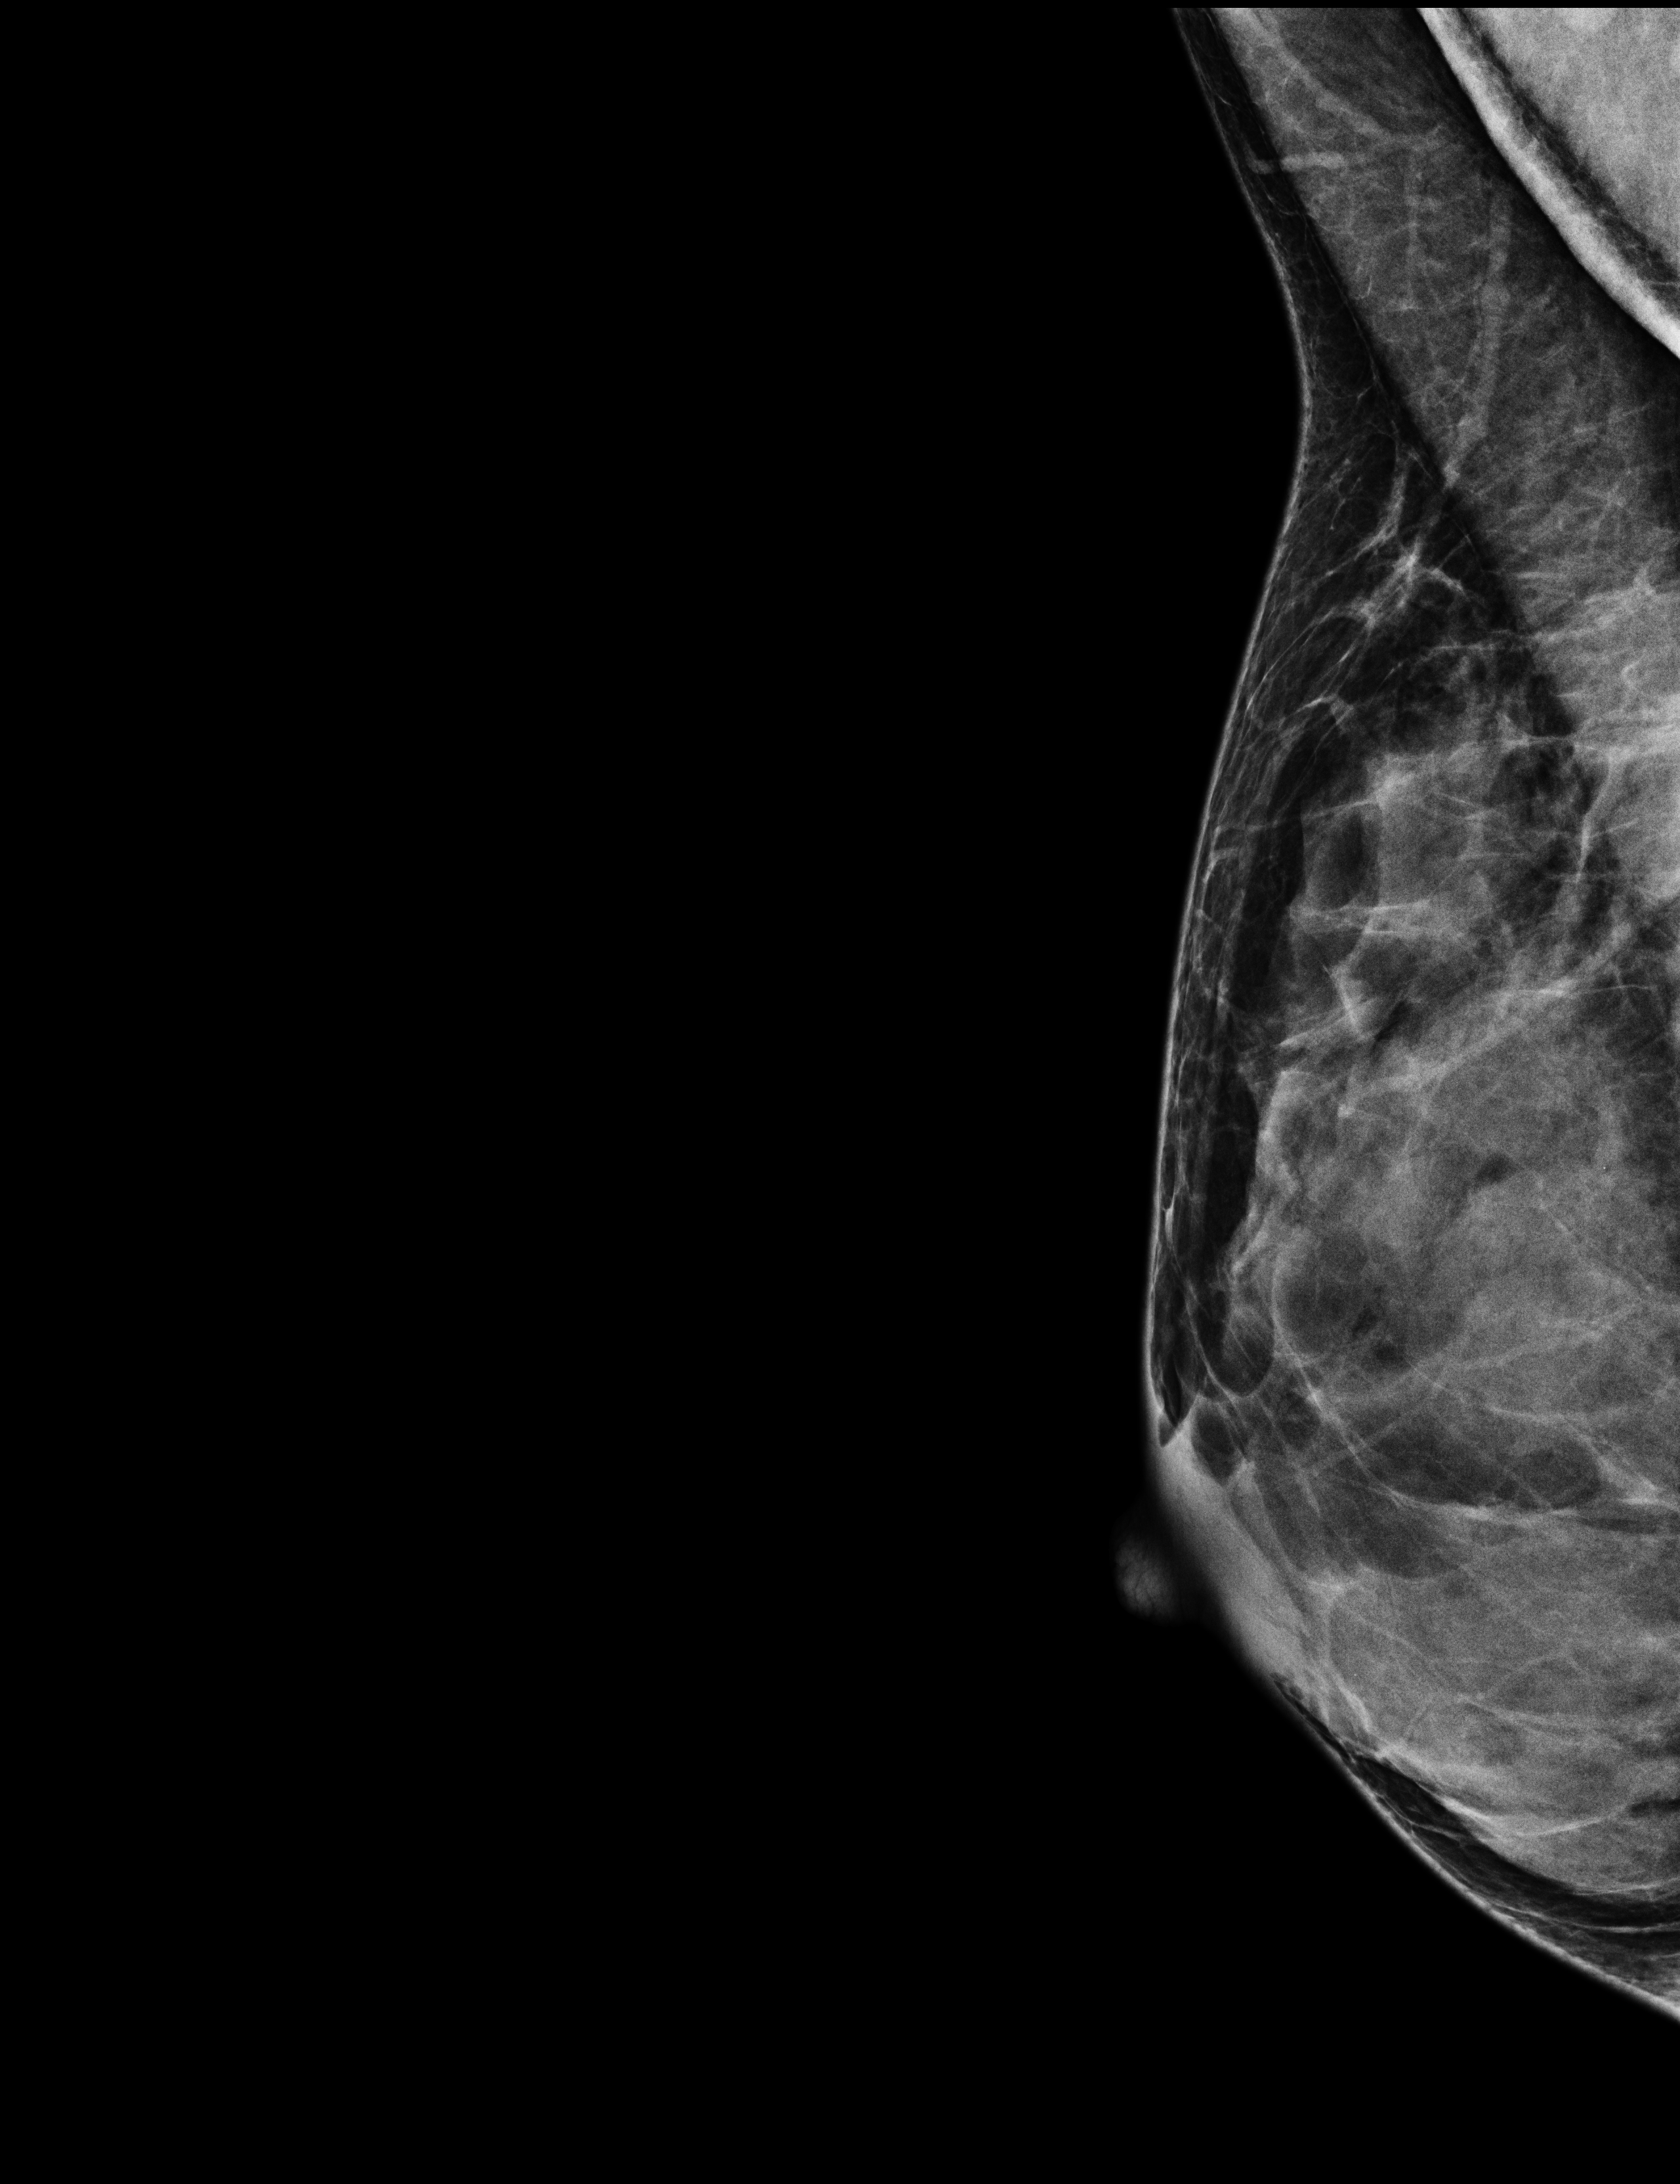
Full-field digital mammogram (FFDM), right breast, MLO view, annual screening mammography examination. Patient aged 42 years (female).
BI-RADS breast density category at the screening exam (both breasts, scale 1–4): 4.